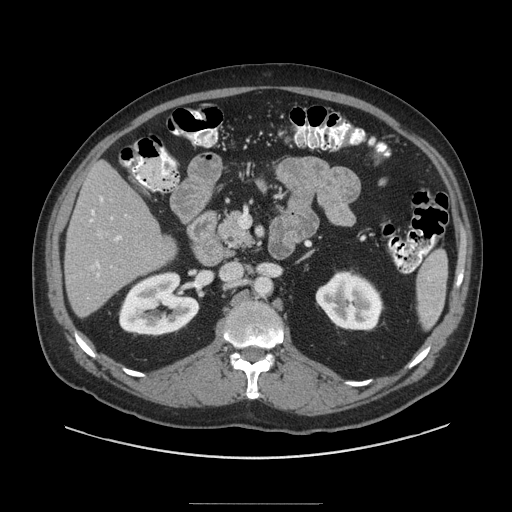
Contrast-enhanced abdominal CT (liver protocol), one axial slice; position 42 of 91 along the scan axis; reconstruction kernel STANDARD; soft-tissue window (W 400 / L 40 HU); 512 × 512 image matrix. From the clinical record (not read from this slice): diagnosis: hepatocellular carcinoma (patient treated with transarterial chemoembolisation; whether this scan precedes or follows treatment is not stated here); TNM stage (as recorded): Stage-I; Child-Pugh class: A; tumour nodularity: uninodular; tumour size: 4 cm.
Annotated regions visible in this slice (semi-automatically segmented with operator editing):
- liver parenchyma outside the tumour (the mass and vessels are separate outlines, so this box may not span the whole liver): box from (x=64, y=161) to (x=176, y=316) px
- liver vessels: (x=90, y=197)–(x=122, y=277)